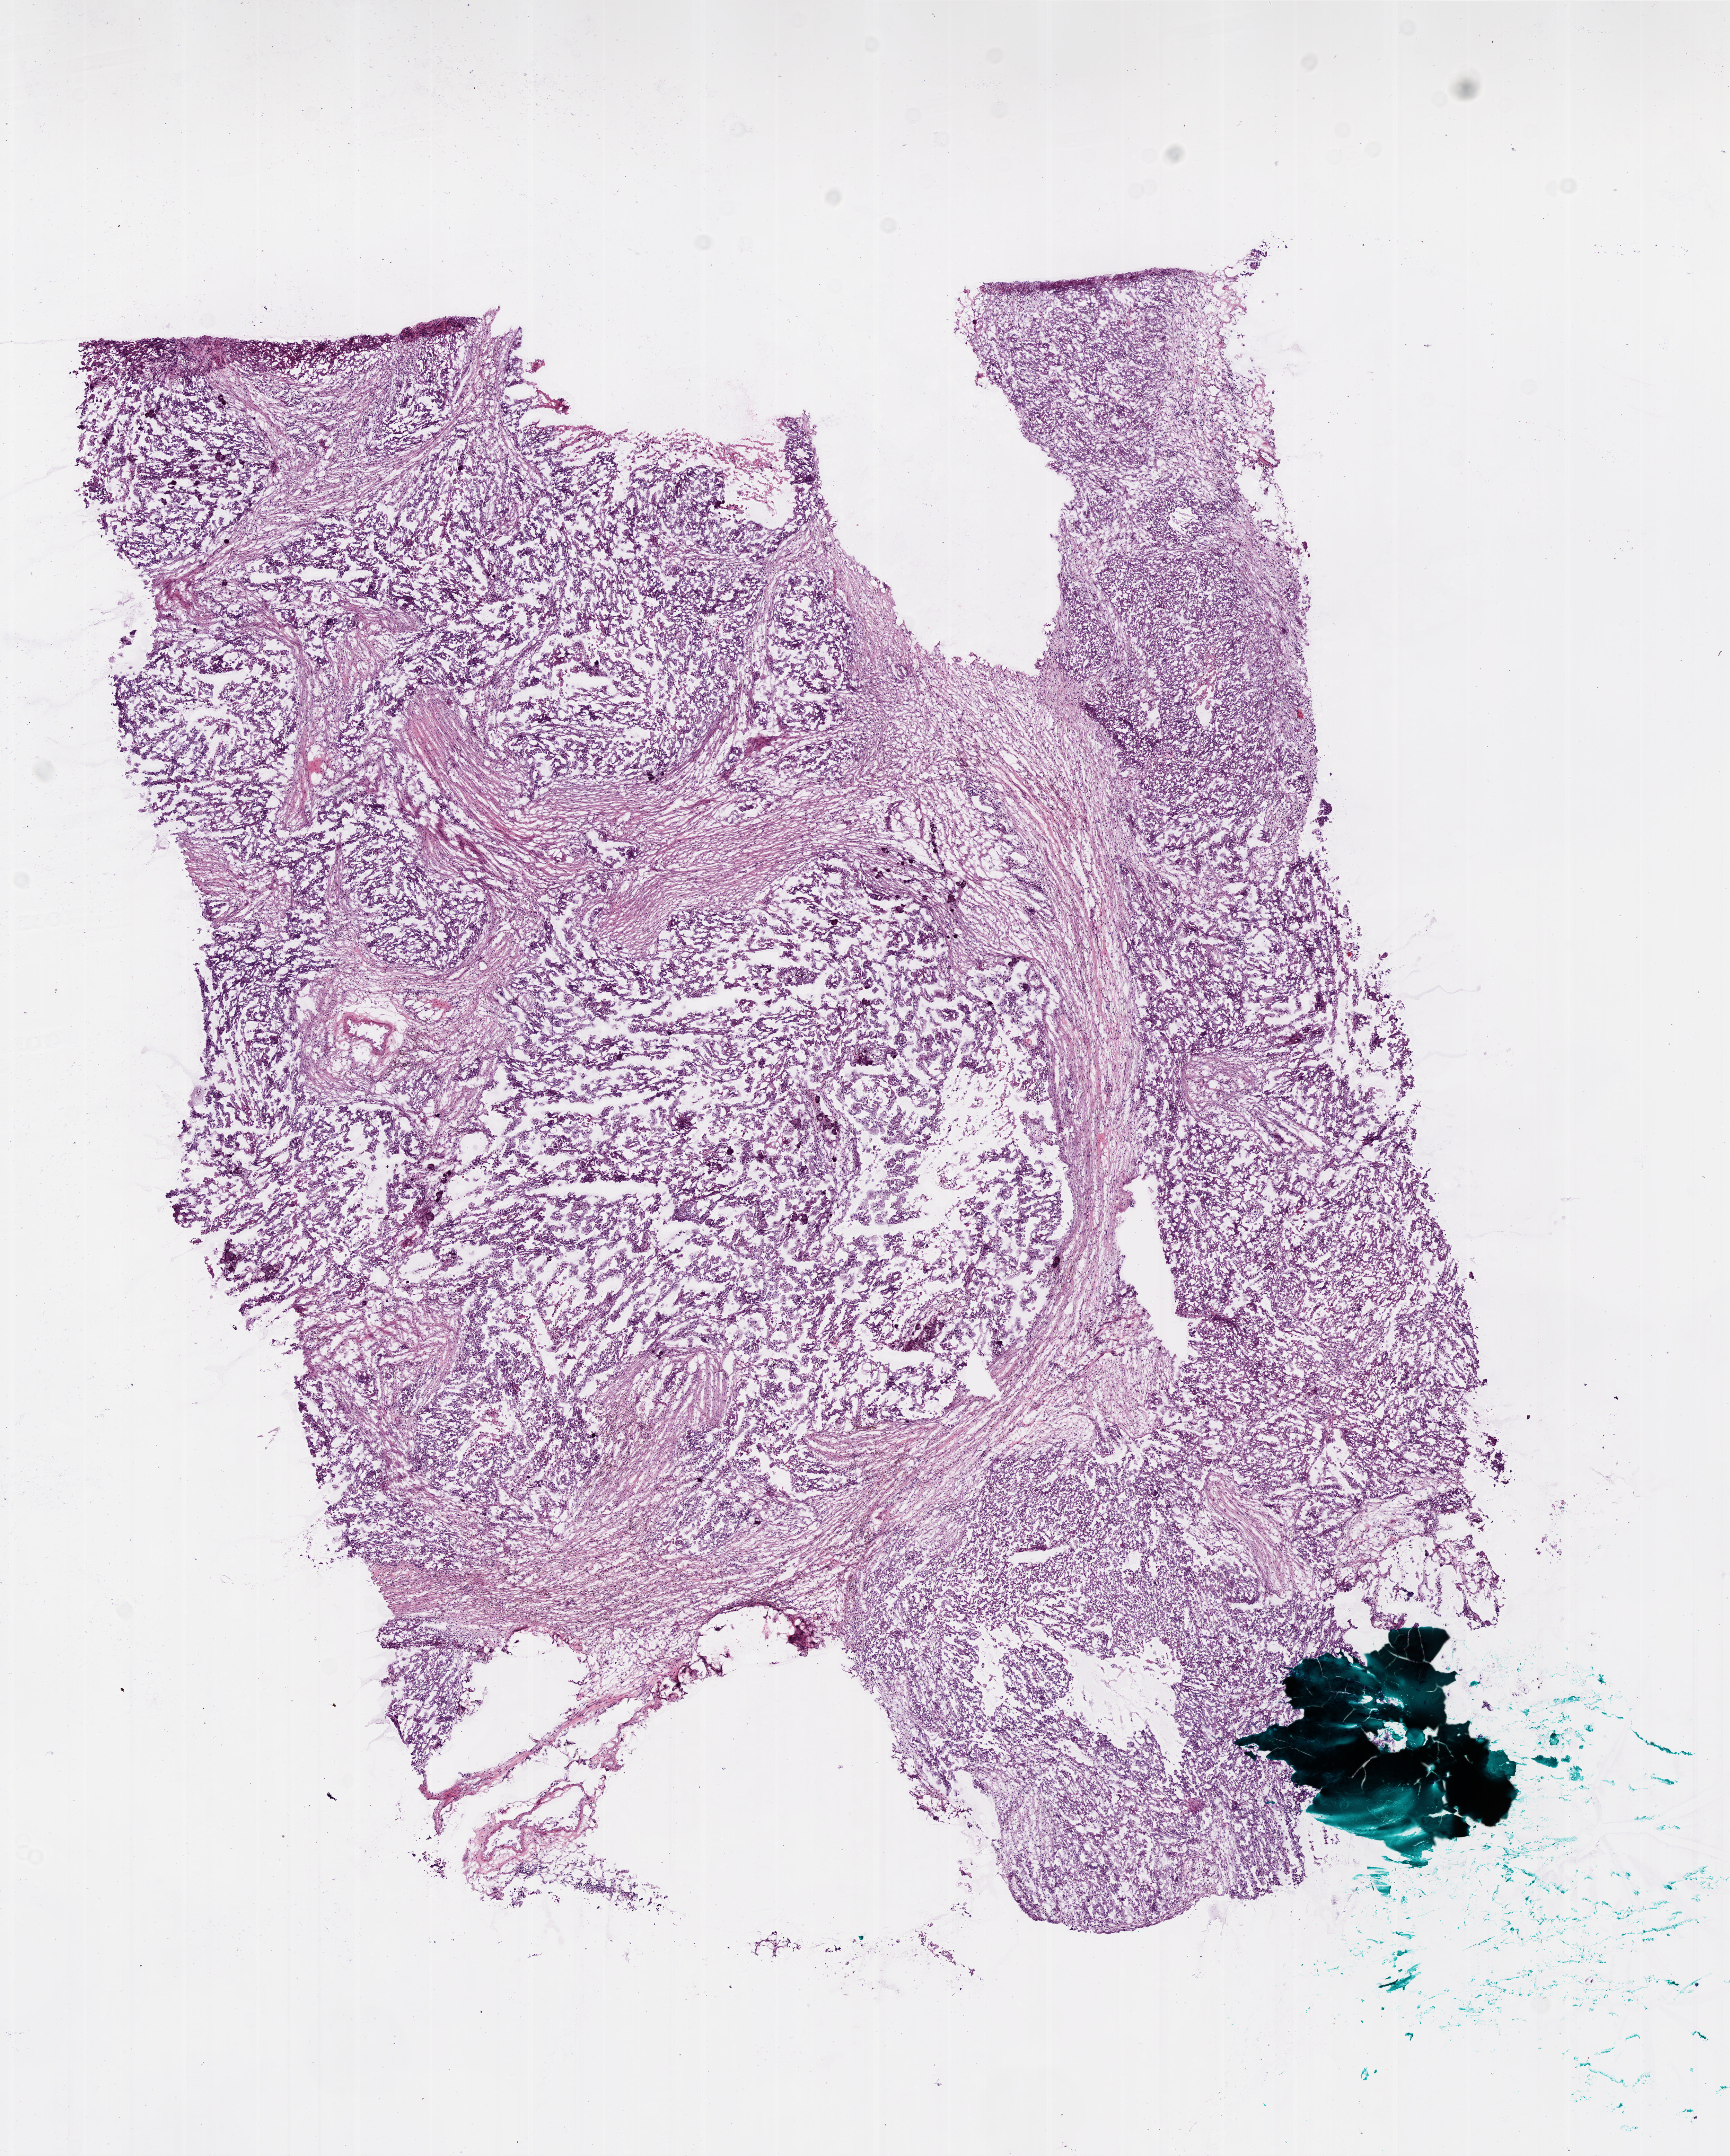
Hematoxylin and eosin (H&E) stained whole-slide image, whole scanned area (about 10.0 x 12.5 mm, slide scanned at 20x) shown as a low-resolution overview; frozen section from the bottom of the tissue portion; ovary, primary tumour sample. Female, age 67 years at initial diagnosis. Histologic grade: G3 (poorly differentiated). Composition of this section per pathologist review: tumour cells 68%, tumour nuclei 70%, normal cells 30%, stromal cells 0%, necrosis 2%.
* FIGO stage: IIIC
* pathologic diagnosis: Serous cystadenocarcinoma, NOS